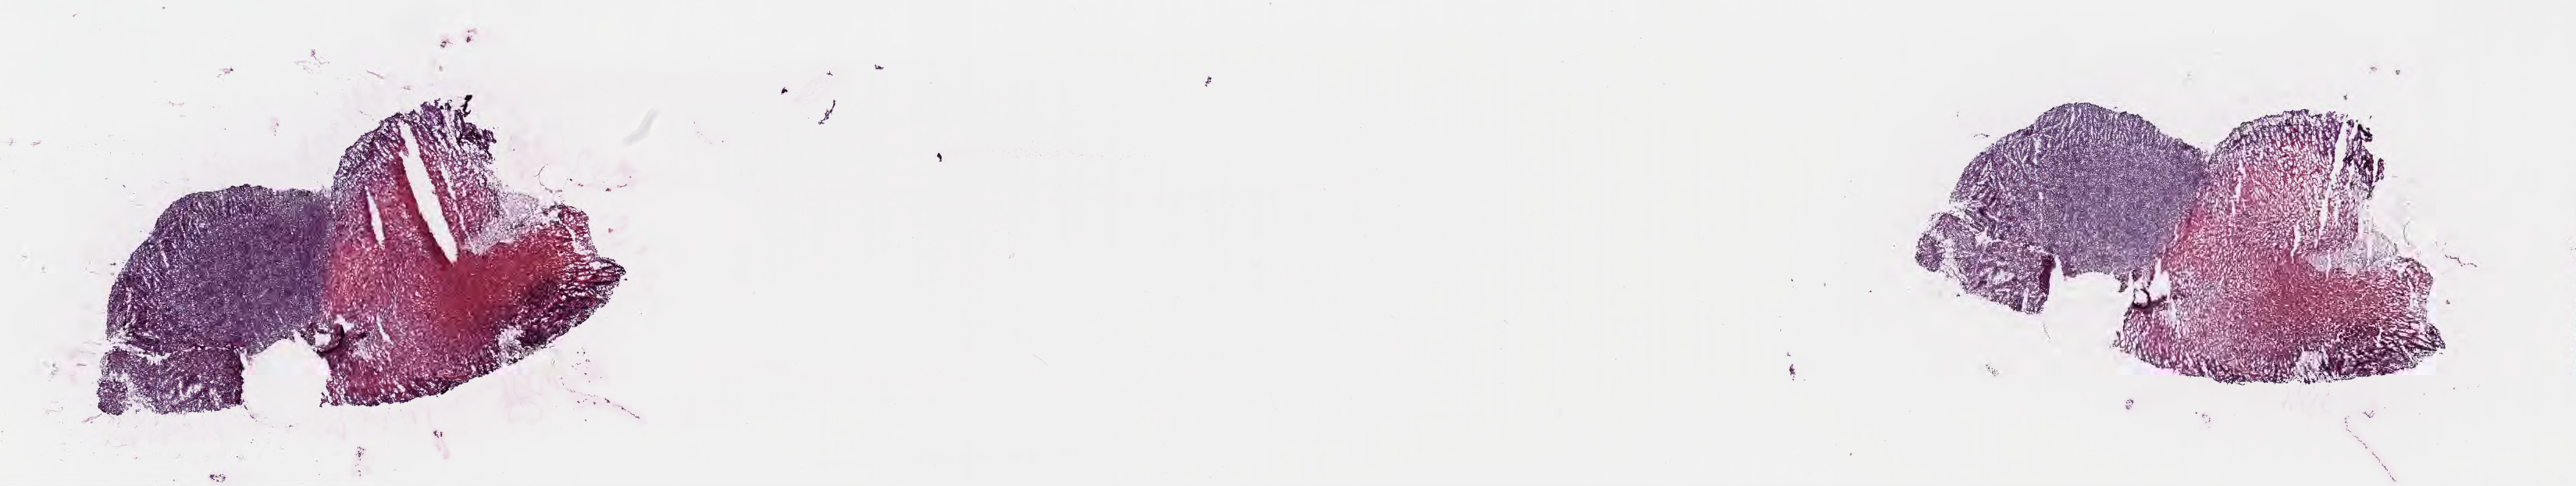
Digitized H&E-stained section — shown as a low-resolution overview of the whole scanned area (about 26.7 x 5.0 mm), frozen section, primary tumor, anatomic site: cranium. Patient male; 11 years old. Composition of this section per pathologist review: tumor cells 45%, tumor nuclei 90%, stromal cells 5%, necrosis 50%, normal cells 0%. Infiltration values recorded for this section: lymphocyte infiltration 50%, monocyte infiltration 30%, neutrophil infiltration 5%.
Ann Arbor stage (patient): Stage III. Diagnosis: Diffuse large B-cell lymphoma, NOS.